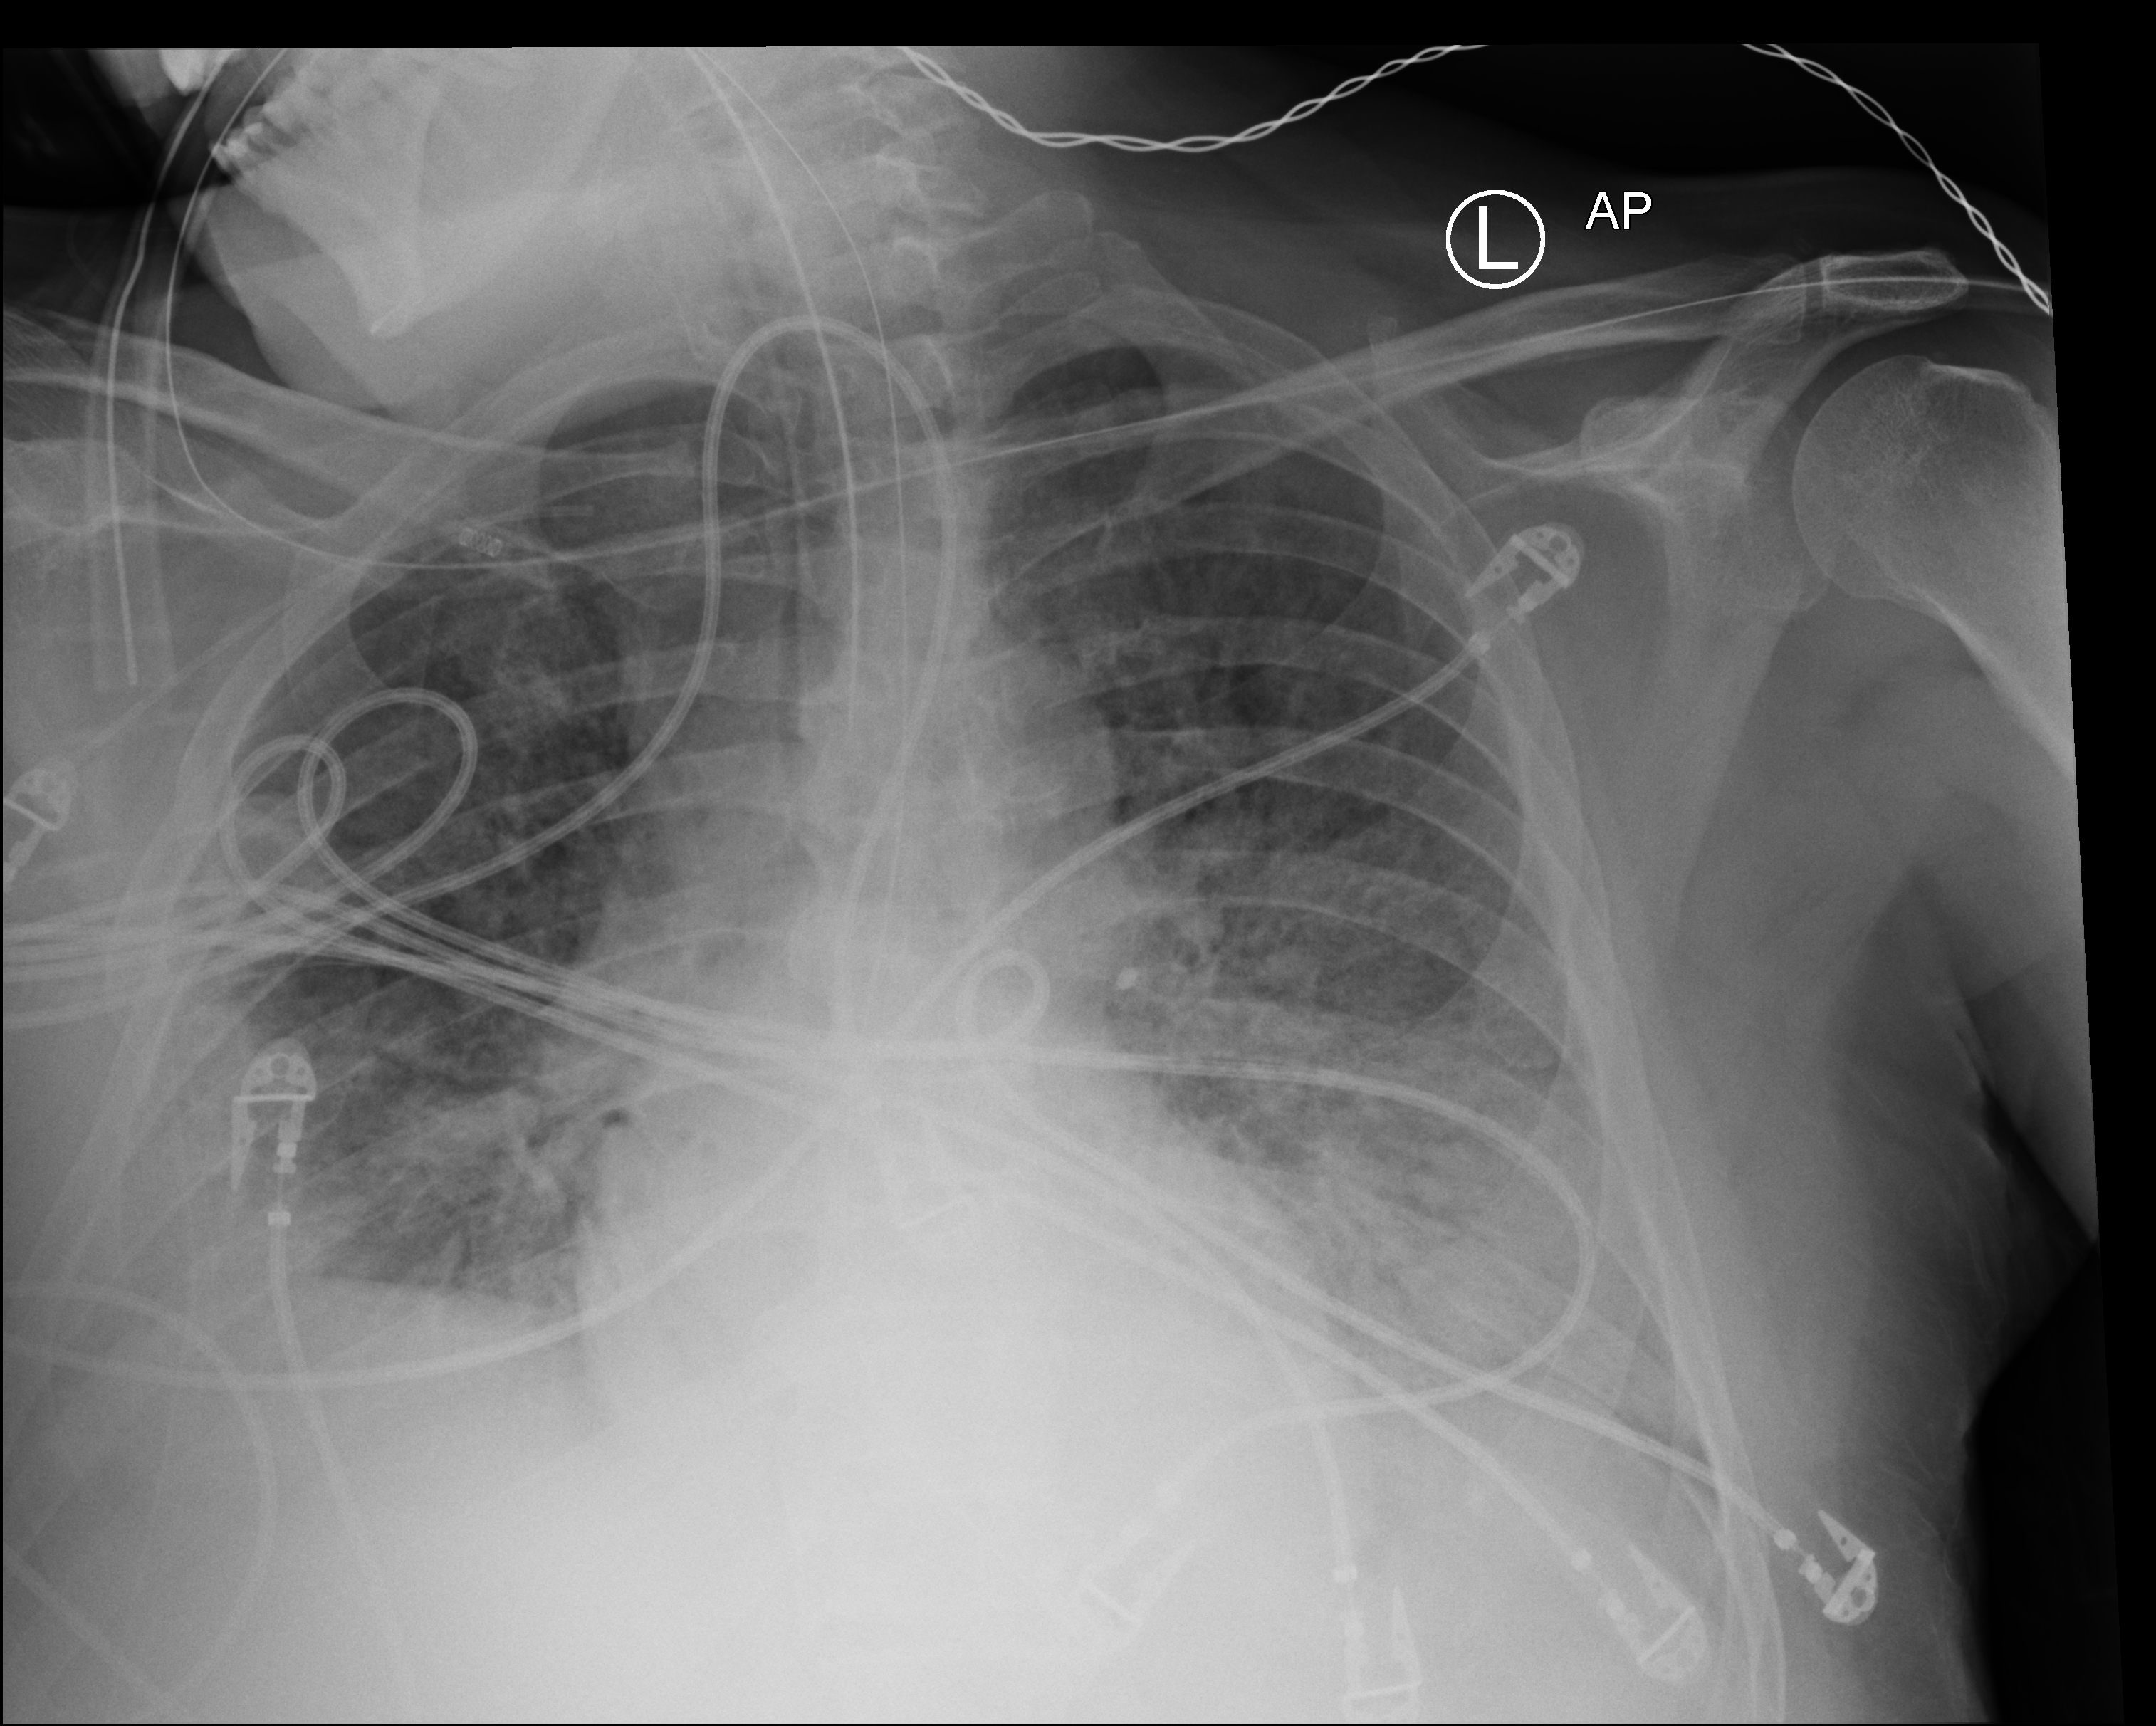
Portable chest radiograph, anteroposterior (AP) projection. Patient hospitalised with COVID-19; male, aged 60–74 years.
Hospital-stay facts (about this admission, not read from this image; timing relative to this image not recorded): admitted to intensive care during this hospital stay: yes; chronic kidney disease (admission record): no.